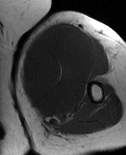
MRI of an extremity soft-tissue mass, one axial slice. Slice 47 of 86 in the series (ordered by position). MR volume resampled by the dataset authors to the PET/CT grid (not the native acquisition matrix). 3.27 mm slice thickness. 126 × 155 image matrix, field of view 123 × 151 mm. Female patient. Case-level facts recorded for this patient, not image findings: histological type: pleiomorphic leiomyosarcoma; grade: high; site of the primary tumour: left biceps.
Annotated regions visible in this slice (expert contour drawn on MRI and transferred to this co-registered scan by the dataset authors):
- gross tumour volume including surrounding oedema: box from (x=20, y=24) to (x=103, y=121) px
- gross tumour volume (mass): (x=20, y=24)–(x=96, y=116)